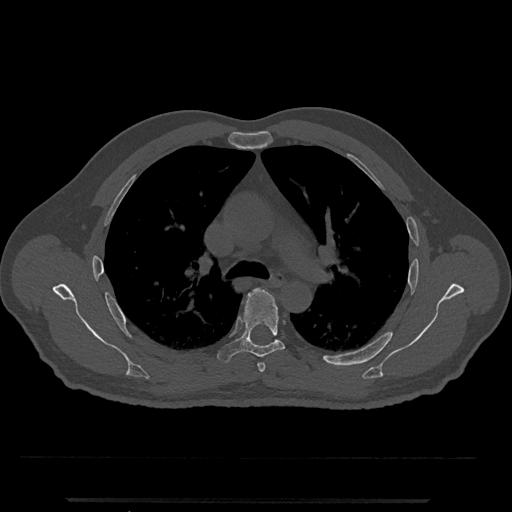
CT including the spine, one axial slice; reconstruction kernel Br40s/3; bone window (W 1800 / L 400 HU); 0.5 mm slice thickness; 512 × 512 image matrix. Patient: male, 63 years. From the clinical record (not read from this slice): primary cancer: prostate.
Structures marked on this image (semi-automatic segmentation, software-assisted and operator-edited):
- T5 vertebra: bounding box <217,288,285,363> (left, top, right, bottom; pixels)